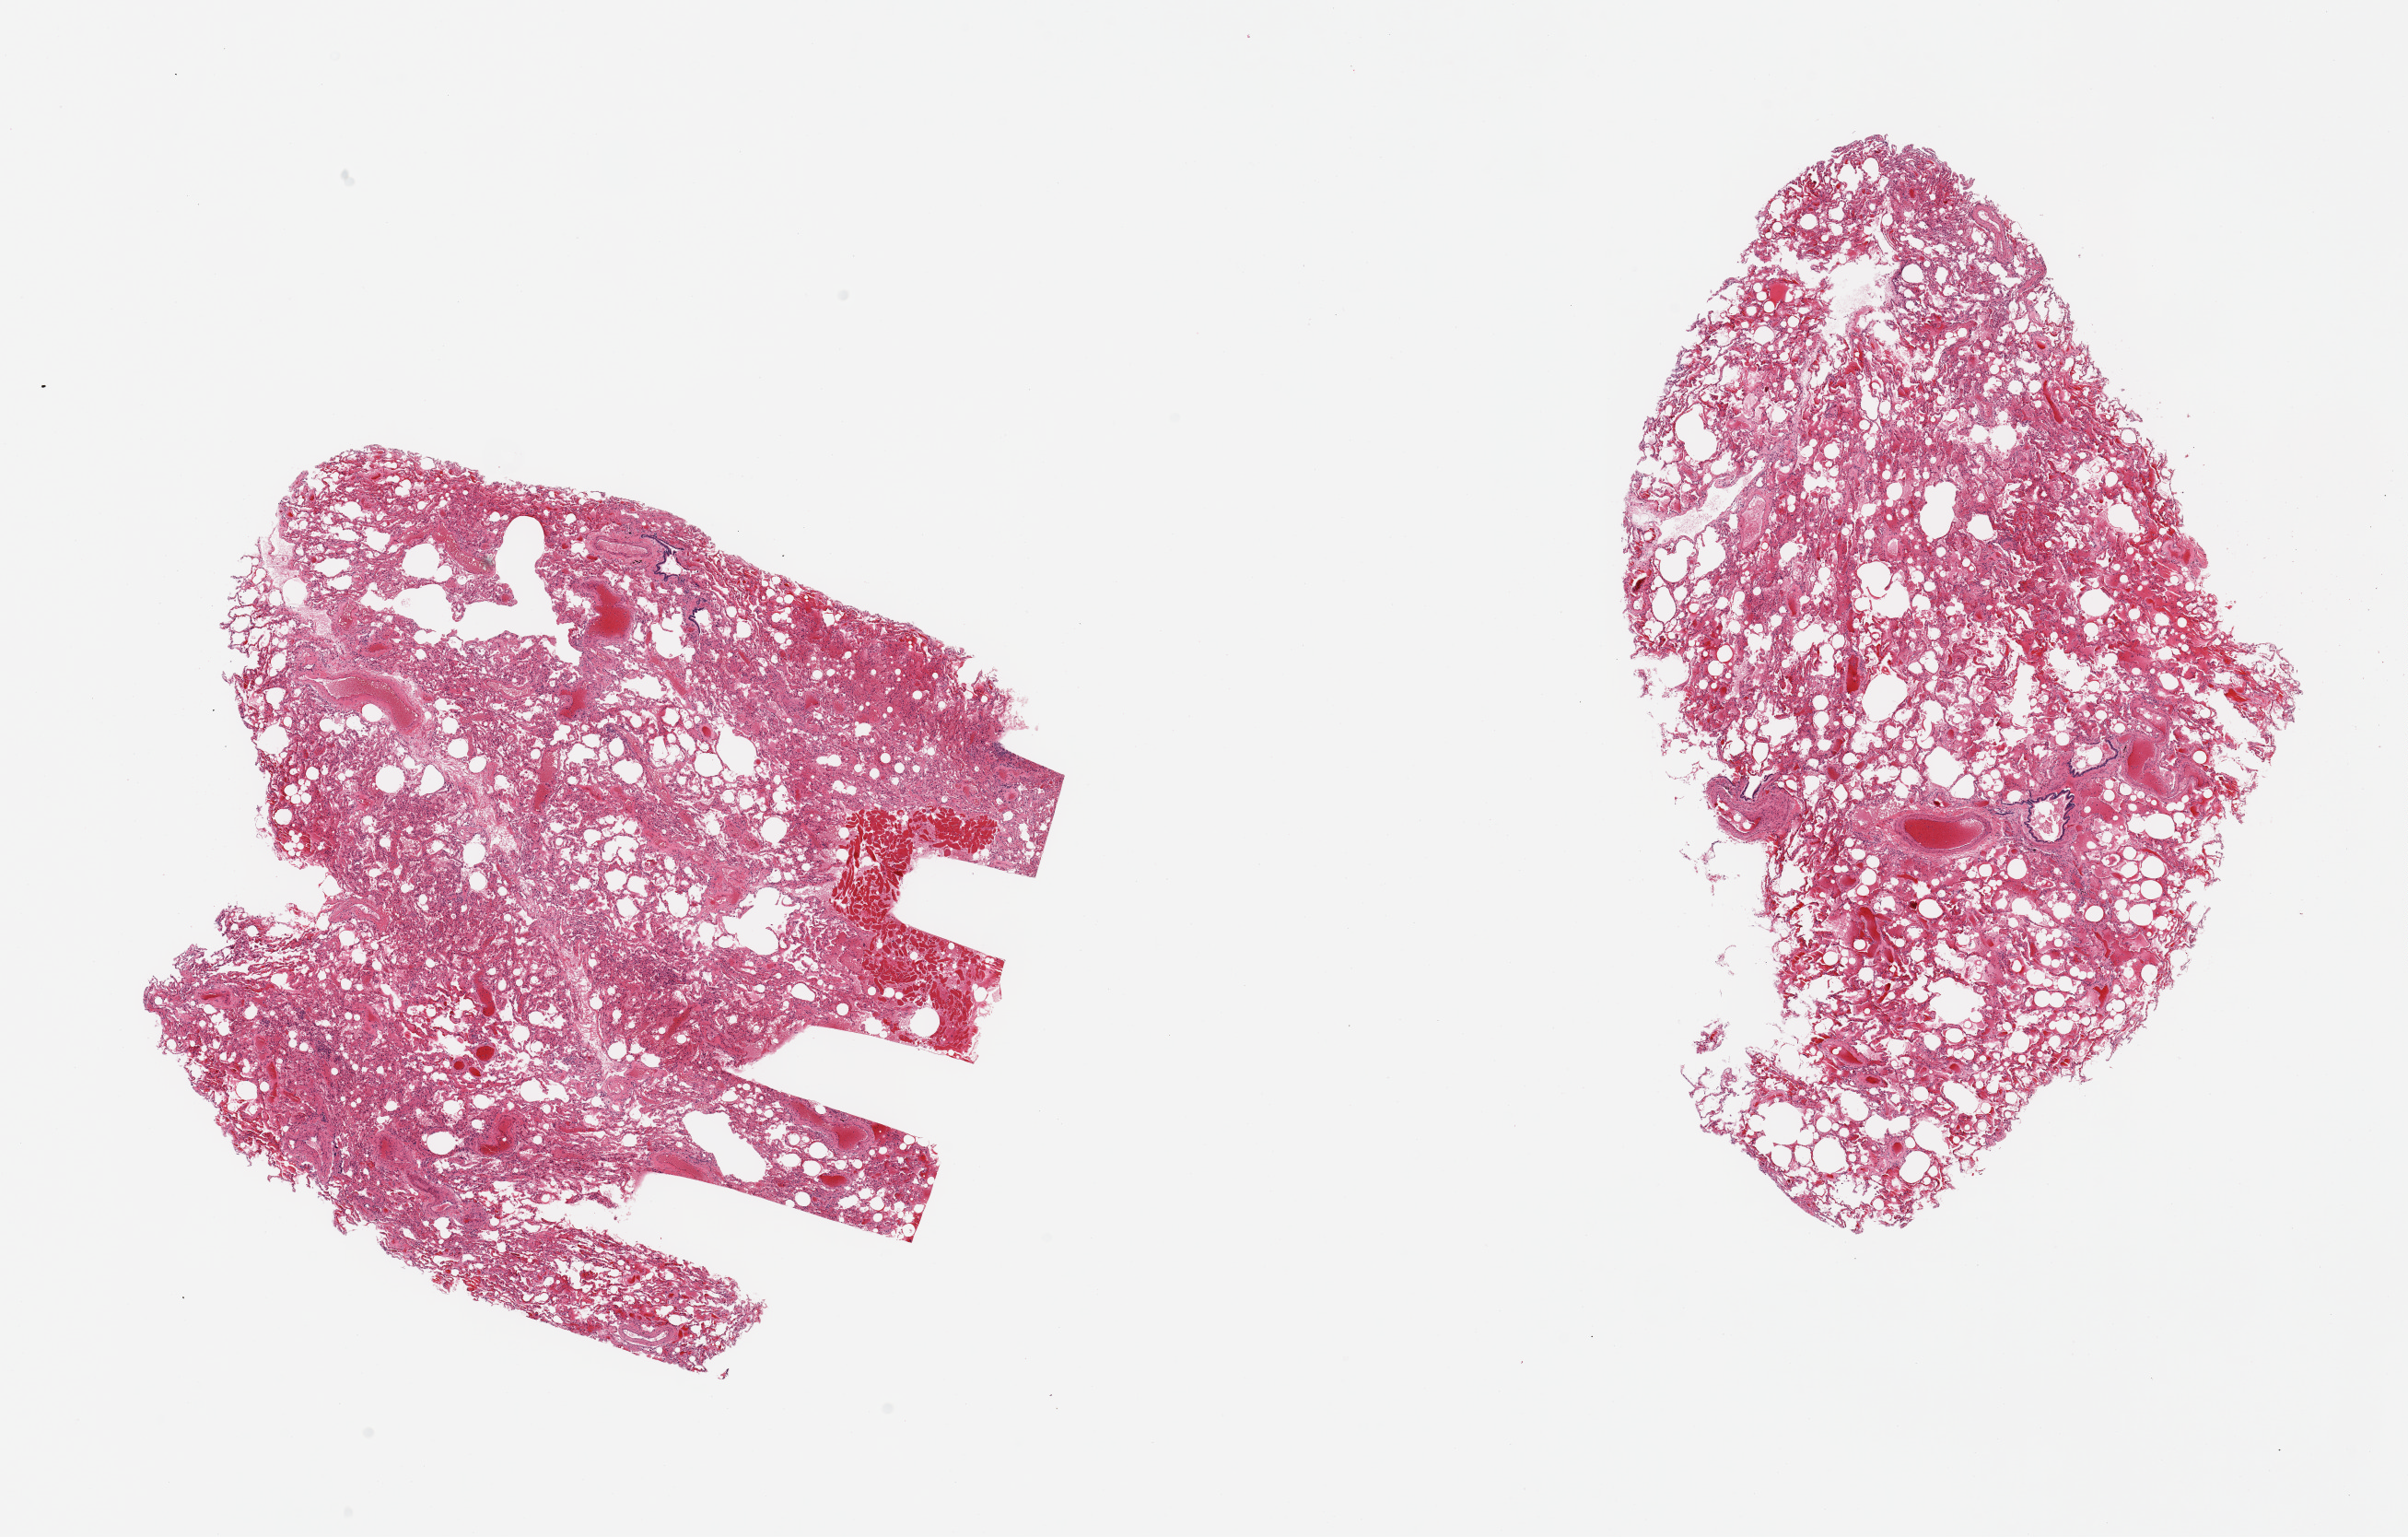
Hematoxylin and eosin (H&E) whole-slide image — a low-resolution overview of the entire scanned area, about 20.7 x 13.2 mm (slide scanned at 20x), PAXgene-fixed paraffin-embedded (PFPE) section, section of lung (target tissue), donor tissue sample.
• pathologist's review note for this sample: 2 pieces; patchy alveolar hemorrhage; skeletal muscle carry-over (2x1.5mm-marked)